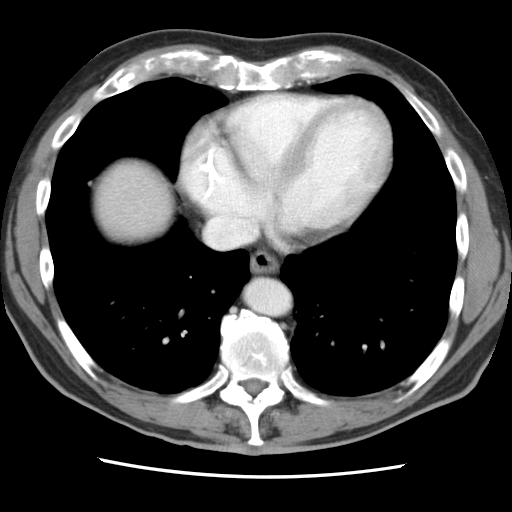
Contrast-enhanced abdominal CT, one axial slice; position 82 of 83 along the scan axis; 120 kVp; intravenous contrast given; soft-tissue window (W 400 / L 40 HU); 512 × 512 image matrix. Male patient, age 69 years. Case-level facts recorded for this patient, not image findings: diagnosis: colorectal cancer liver metastases, imaged before liver resection; multiple liver metastases: yes; largest metastasis: 3.5 cm.
Structures marked on this image (expert manual segmentation):
- liver: bounding box <90,160,173,241> (left, top, right, bottom; pixels)
- planned liver remnant (the part of the liver to remain after resection): <90,162,174,239>